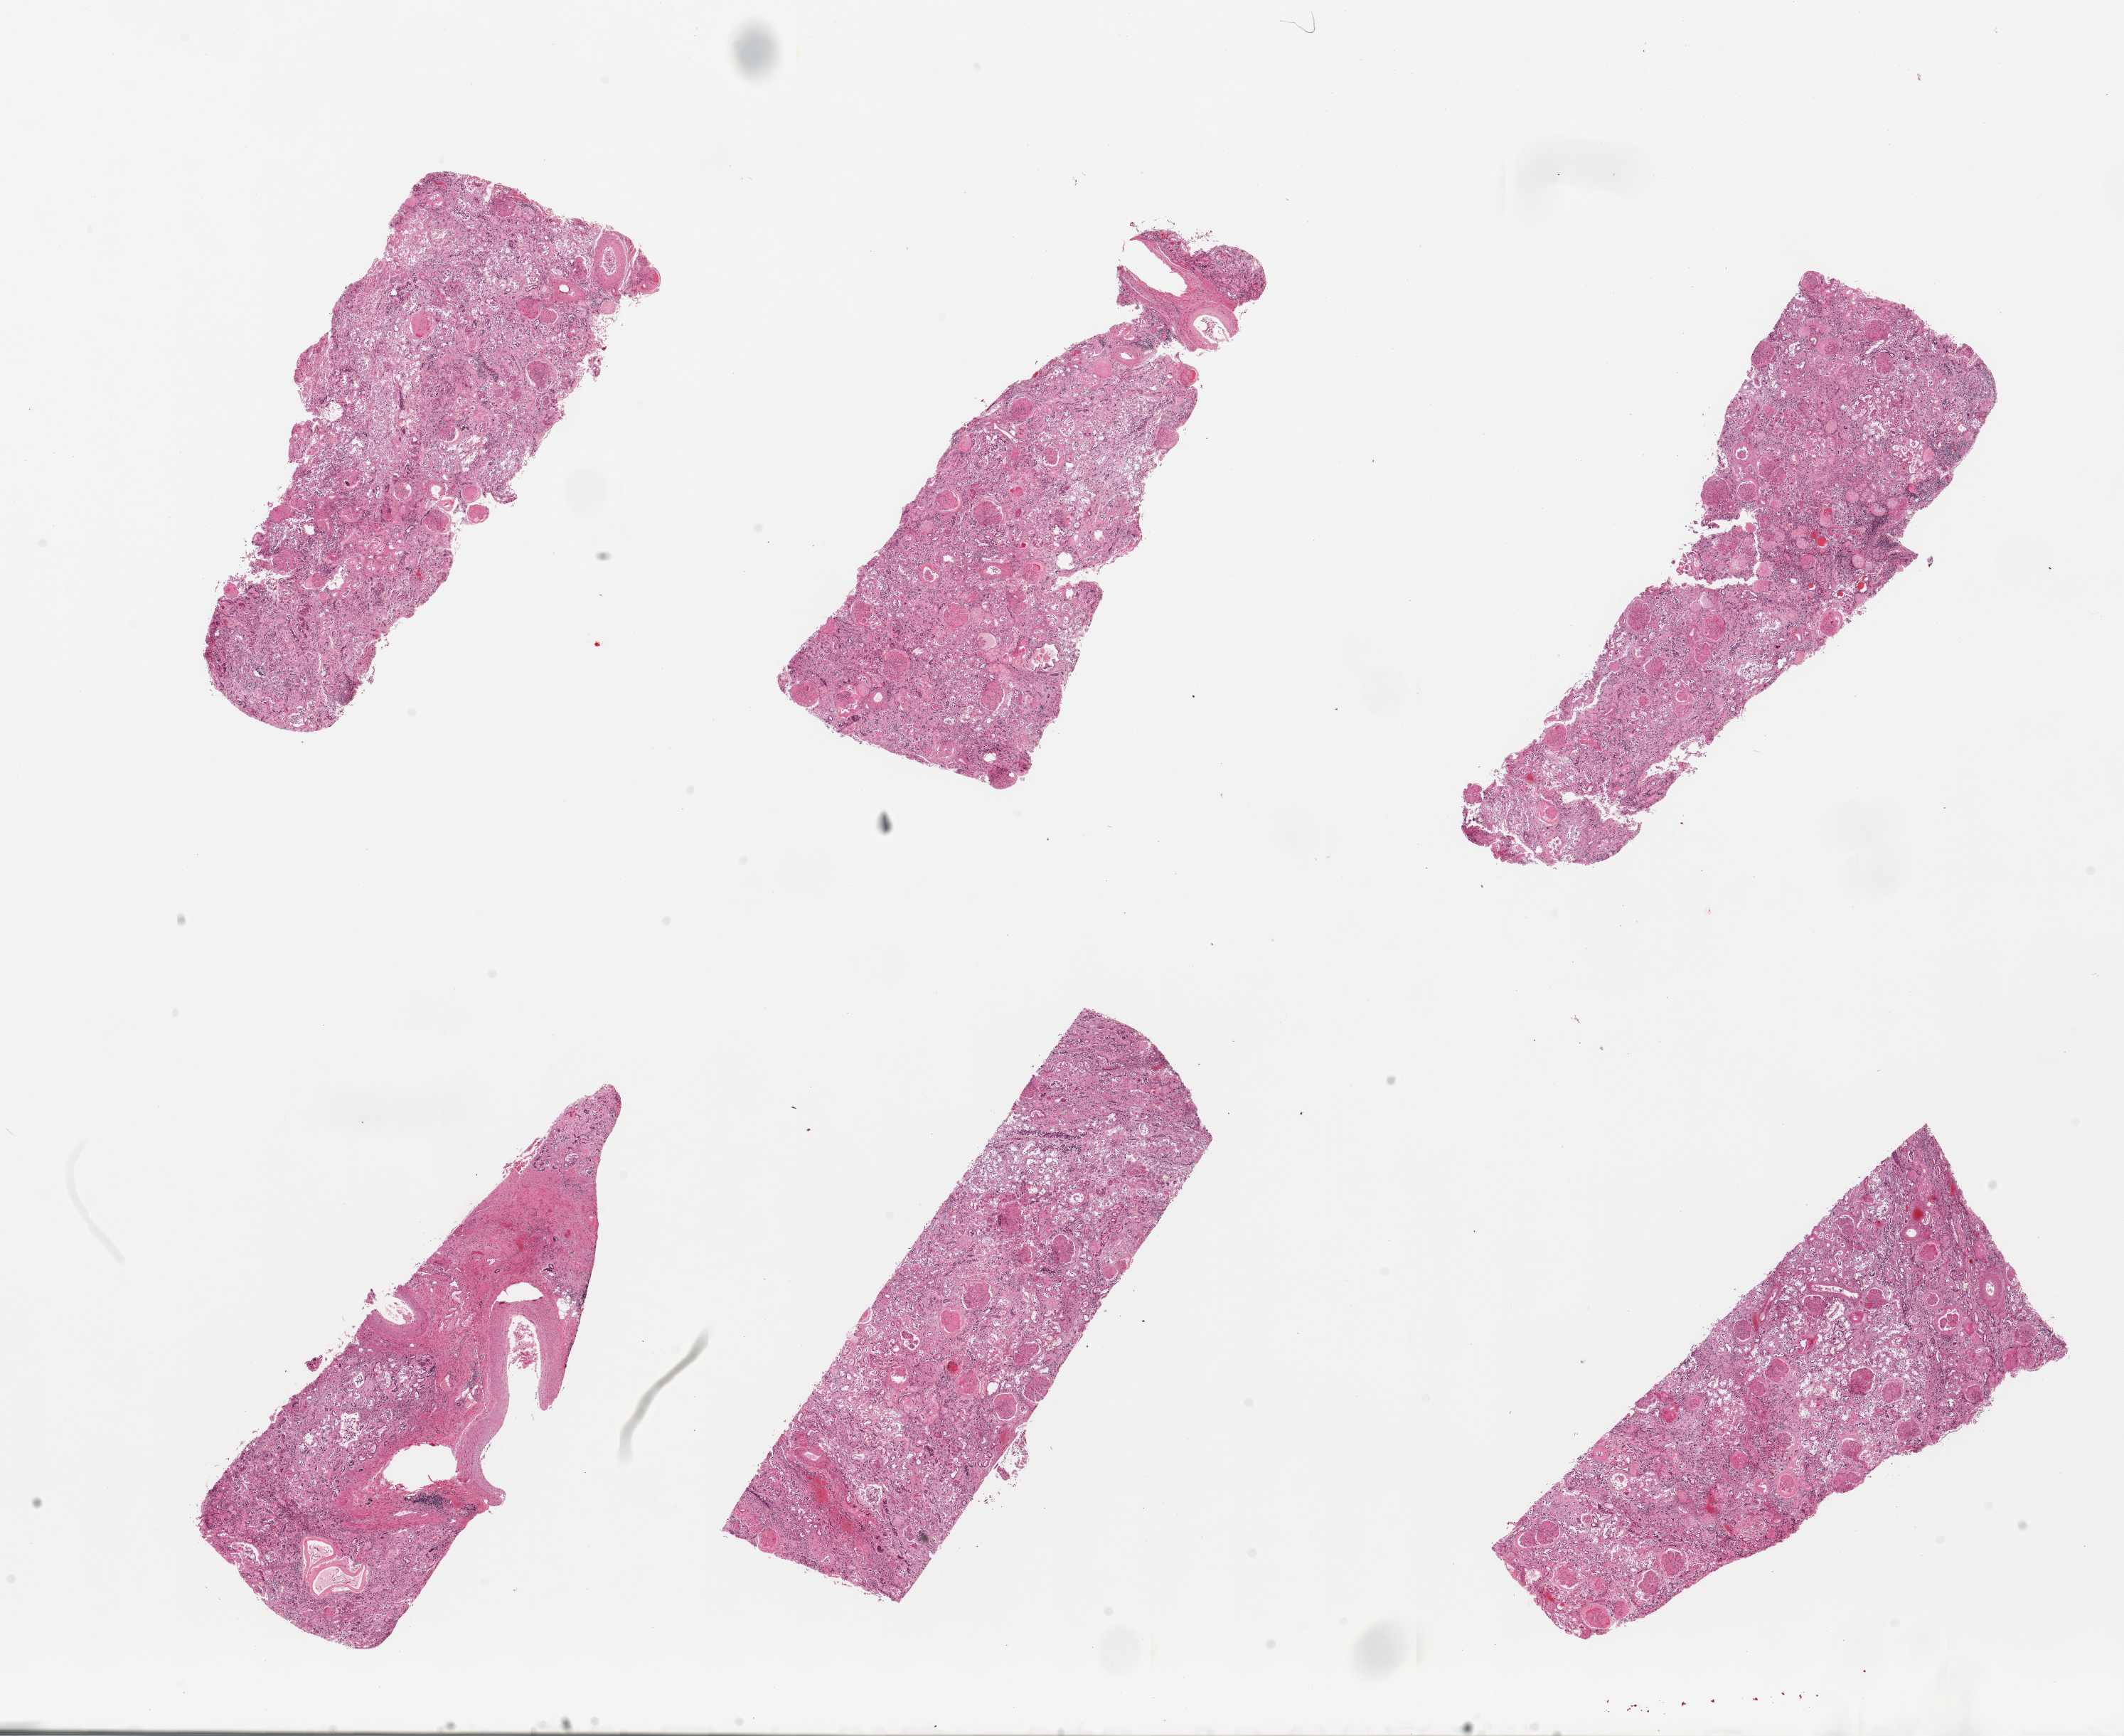
Whole-slide image, hematoxylin and eosin (H&E) stain, whole scanned area (about 23.6 x 19.3 mm, from a 20x scan) shown as a low-resolution overview, PAXgene-fixed, paraffin-embedded tissue, sampled site (target tissue): renal cortex, donor tissue sample. Female donor.
Review note (as recorded): 6 pieces, glmeruli present, tubules autolyzed. Marked glomerulosclerosis.